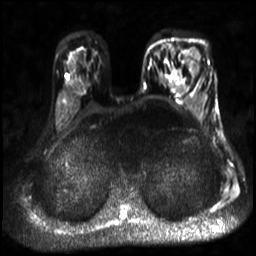
Breast MRI, one axial slice; slice 19 of 30 in the series (ordered by position); diffusion-weighted series; image 2 of 4 stored at this slice position (different b-values; order by instance number); 3 T; 4 mm slice thickness; 256 × 256 image matrix, field of view 320 × 320 mm. Female patient.
Annotated regions visible in this slice (manually delineated by an expert):
- tumour on diffusion-weighted imaging: box from (x=183, y=52) to (x=201, y=76) px